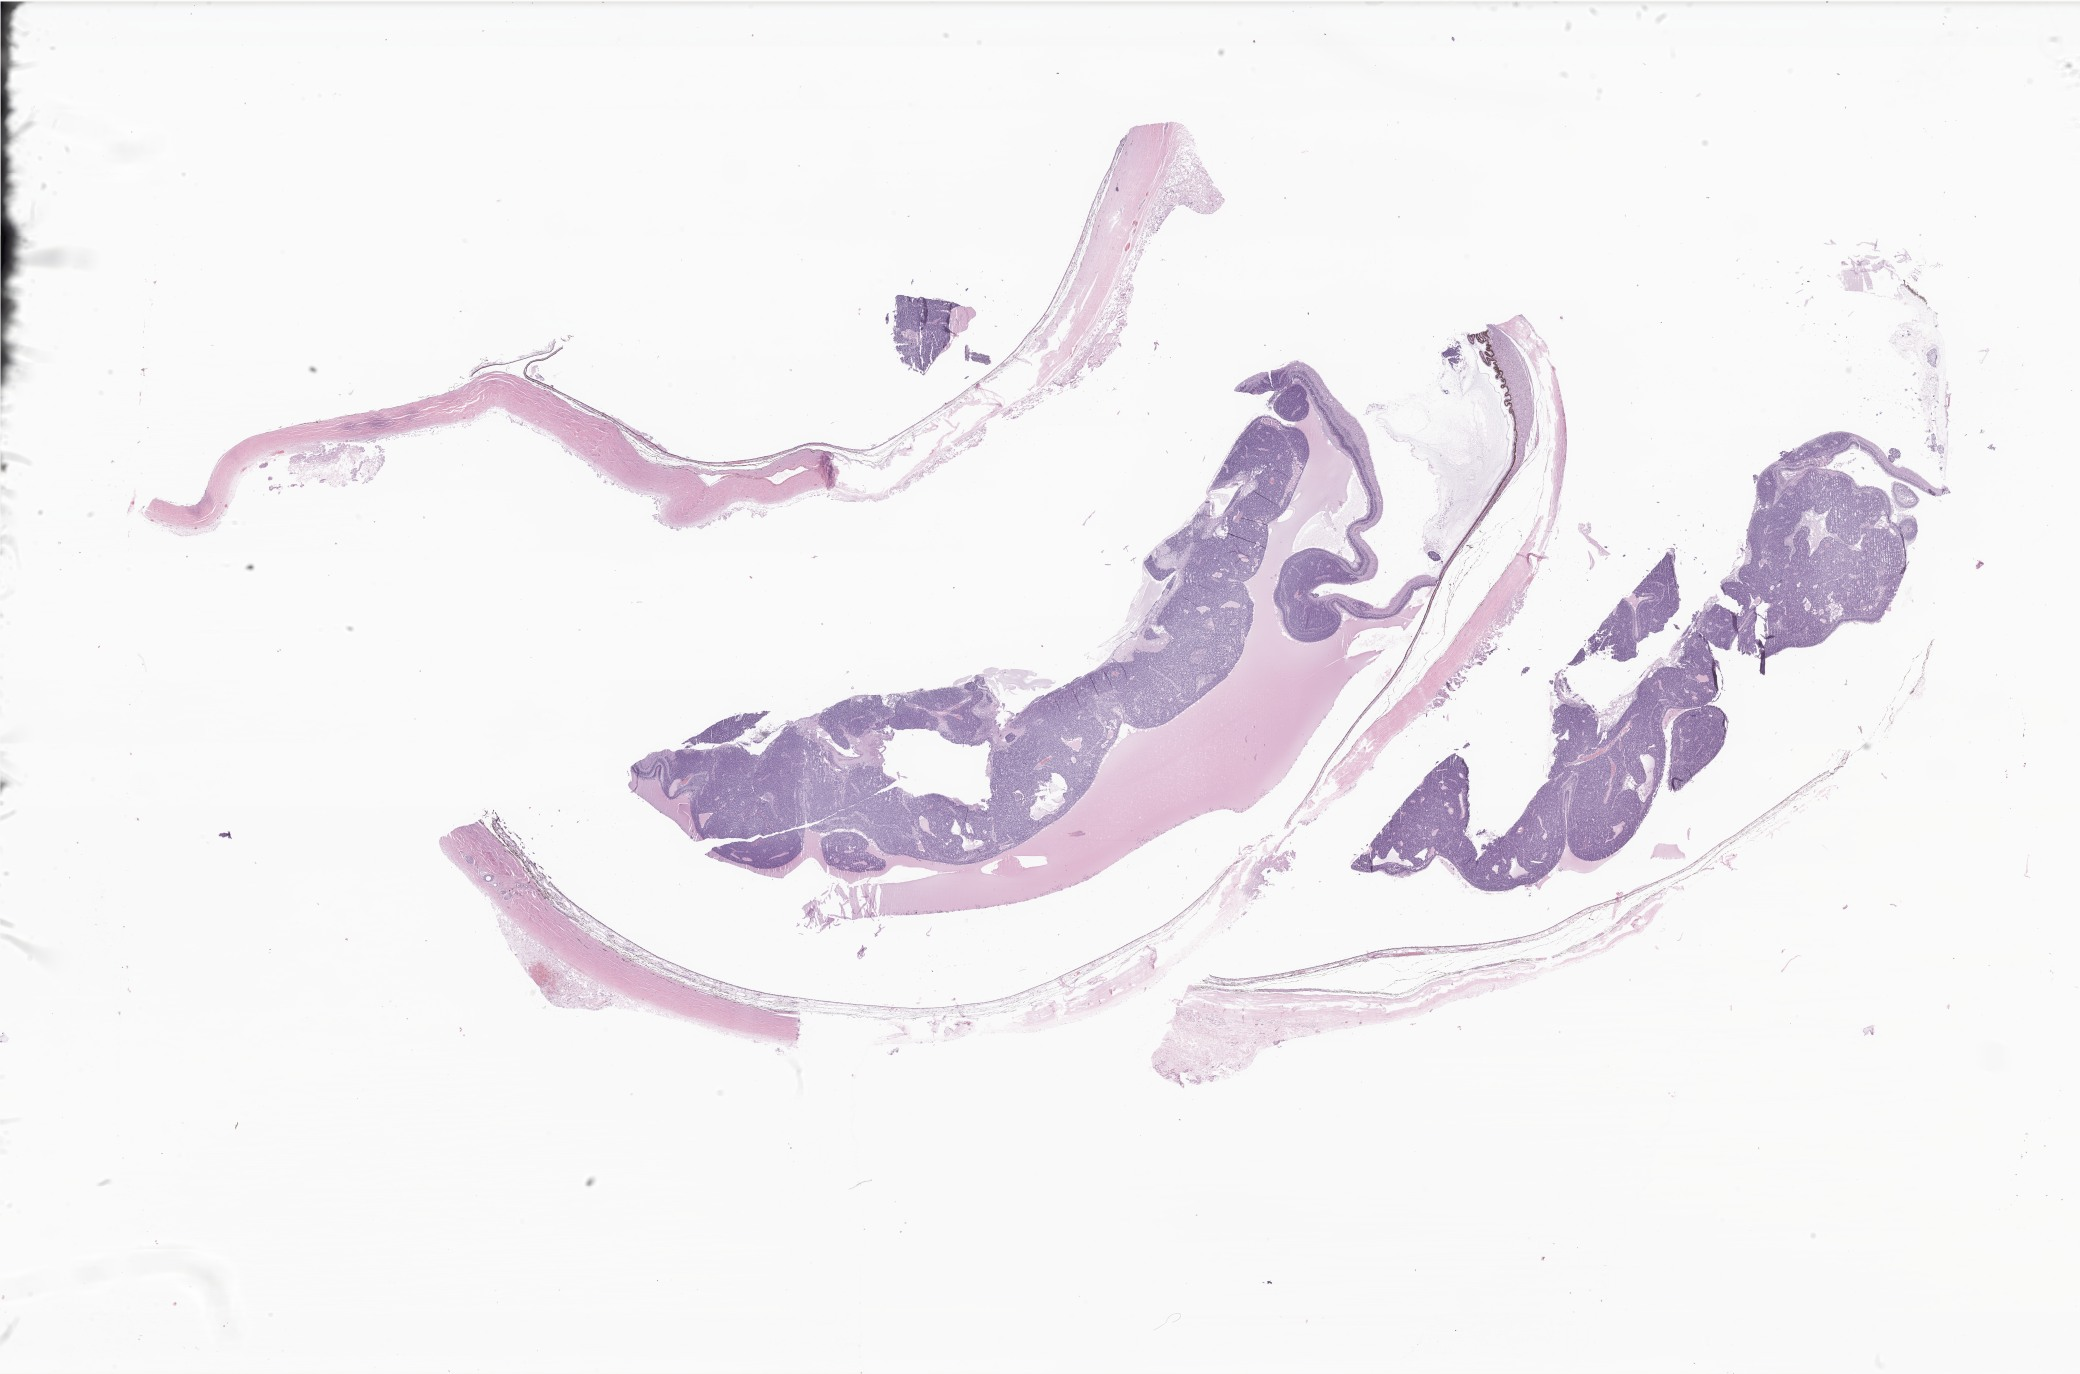
Haematoxylin and eosin whole-slide image of tumor tissue from the retina, low-resolution overview of the scanned area, about 35.1 x 23.2 mm; formalin-fixed paraffin-embedded section. Patient: male, age 815 days (about 2.2 years).
Recorded diagnosis: Retinoblastoma, NOS.